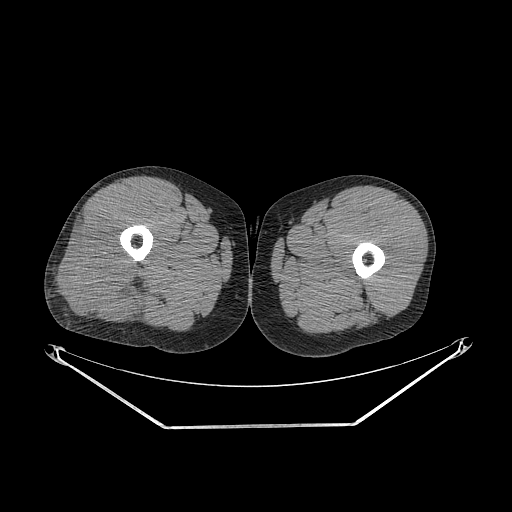
CT of an extremity soft-tissue mass (from a PET/CT study), one axial slice. Position 252 of 267 along the scan axis. Reconstruction kernel STANDARD. Soft-tissue window (W 400 / L 40 HU). 3.75 mm slice thickness. 512 × 512 image matrix. Male patient. From the clinical record (not read from this slice): histological type: poorly differentiated synovial sarcoma; grade: high; site of the primary tumour: right buttock.
Annotated regions visible in this slice (expert contour drawn on MRI and transferred to this co-registered scan by the dataset authors):
- gross tumour volume including surrounding oedema: bounding box [x1, y1, x2, y2] px = [60, 219, 149, 321]
- gross tumour volume (mass): [60, 219, 145, 321]